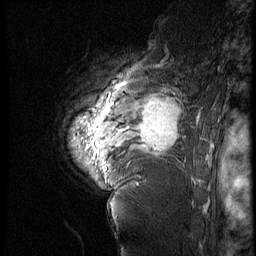
Breast MRI (dynamic contrast-enhanced), one sagittal slice; position 49 of 60 along the scan axis; 4 images stored at this slice position (order not interpretable as contrast timing); 1.5 T; TE 4.2 ms, TR 9 ms; 2.5 mm slice thickness; 256 × 256 image matrix, field of view 180 × 180 mm. Female patient, age 56 years. From the clinical record (not read from this slice): setting: breast cancer imaged before/during neoadjuvant chemotherapy; receptor status: HER2-positive.
Structures marked on this image (semi-automatically segmented with operator editing):
- analysis volume of interest (the breast-tissue region the enhancement analysis was run in; not a lesion): bounding box [x1, y1, x2, y2] px = [82, 83, 199, 177]
- tumour enhancement mask (voxels above the 140 % enhancement threshold inside the analysis volume of interest): [126, 98, 181, 154]